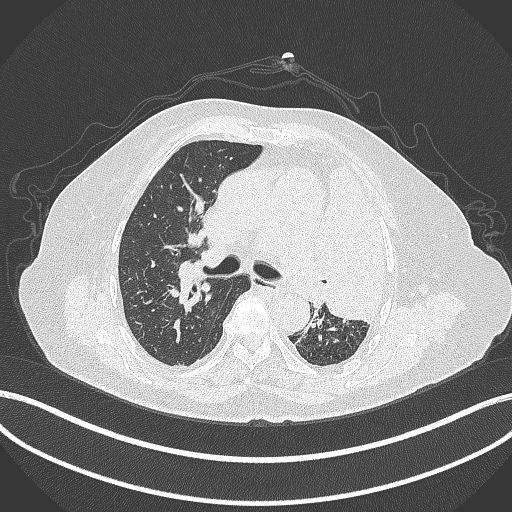
Chest CT, one axial slice. Position 244 of 399 along the scan axis. 120 kVp. Lung window (W 1500 / L -600 HU). 1 mm slice thickness. 512 × 512 image matrix, field of view 400 × 400 mm. Female patient, age 75 years. From the clinical record (not read from this slice): clinical TNM (as recorded): T3 N3 M1.
Outlined on this slice (rectangle marked by the reading radiologist):
- lung tumour (recorded histology: adenocarcinoma): bounding box (x1, y1, x2, y2) in pixels: (310, 164, 391, 328)